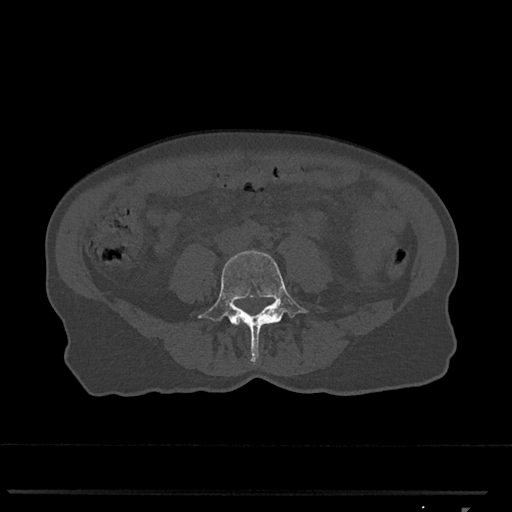
CT including the spine, one axial slice; position 213 of 793 along the scan axis; reconstruction kernel Br40s/3; bone window (W 1800 / L 400 HU); 0.5 mm slice thickness; 512 × 512 image matrix, field of view 380 × 380 mm. Patient: female, 62 years. From the clinical record (not read from this slice): primary cancer: renal.
Annotated regions visible in this slice (semi-automatically segmented with operator editing):
- L4 vertebra: bounding box (x1, y1, x2, y2) in pixels: (198, 250, 308, 362)